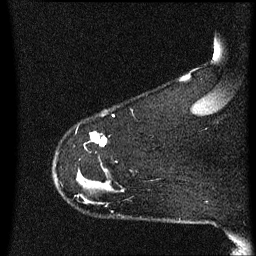
Breast MRI (dynamic contrast-enhanced), one sagittal slice. Slice 53 of 60 in the series (ordered by position). Dynamic contrast-enhanced series, image 2 of 3 at this slice position (ordered by acquisition). 1.5 T. TE 4.2 ms, TR 8.4 ms. 2 mm slice thickness. 256 × 256 image matrix, field of view 200 × 200 mm. Female patient, age 48 years.
Annotated regions visible in this slice (semi-automatically segmented with operator editing):
- analysis volume of interest (the breast-tissue region the enhancement analysis was run in; not a lesion): bounding box (x1, y1, x2, y2) in pixels: (55, 134, 124, 213)
- tumour enhancement mask (voxels above the 70 % enhancement threshold inside the analysis volume of interest): (91, 134, 106, 147)